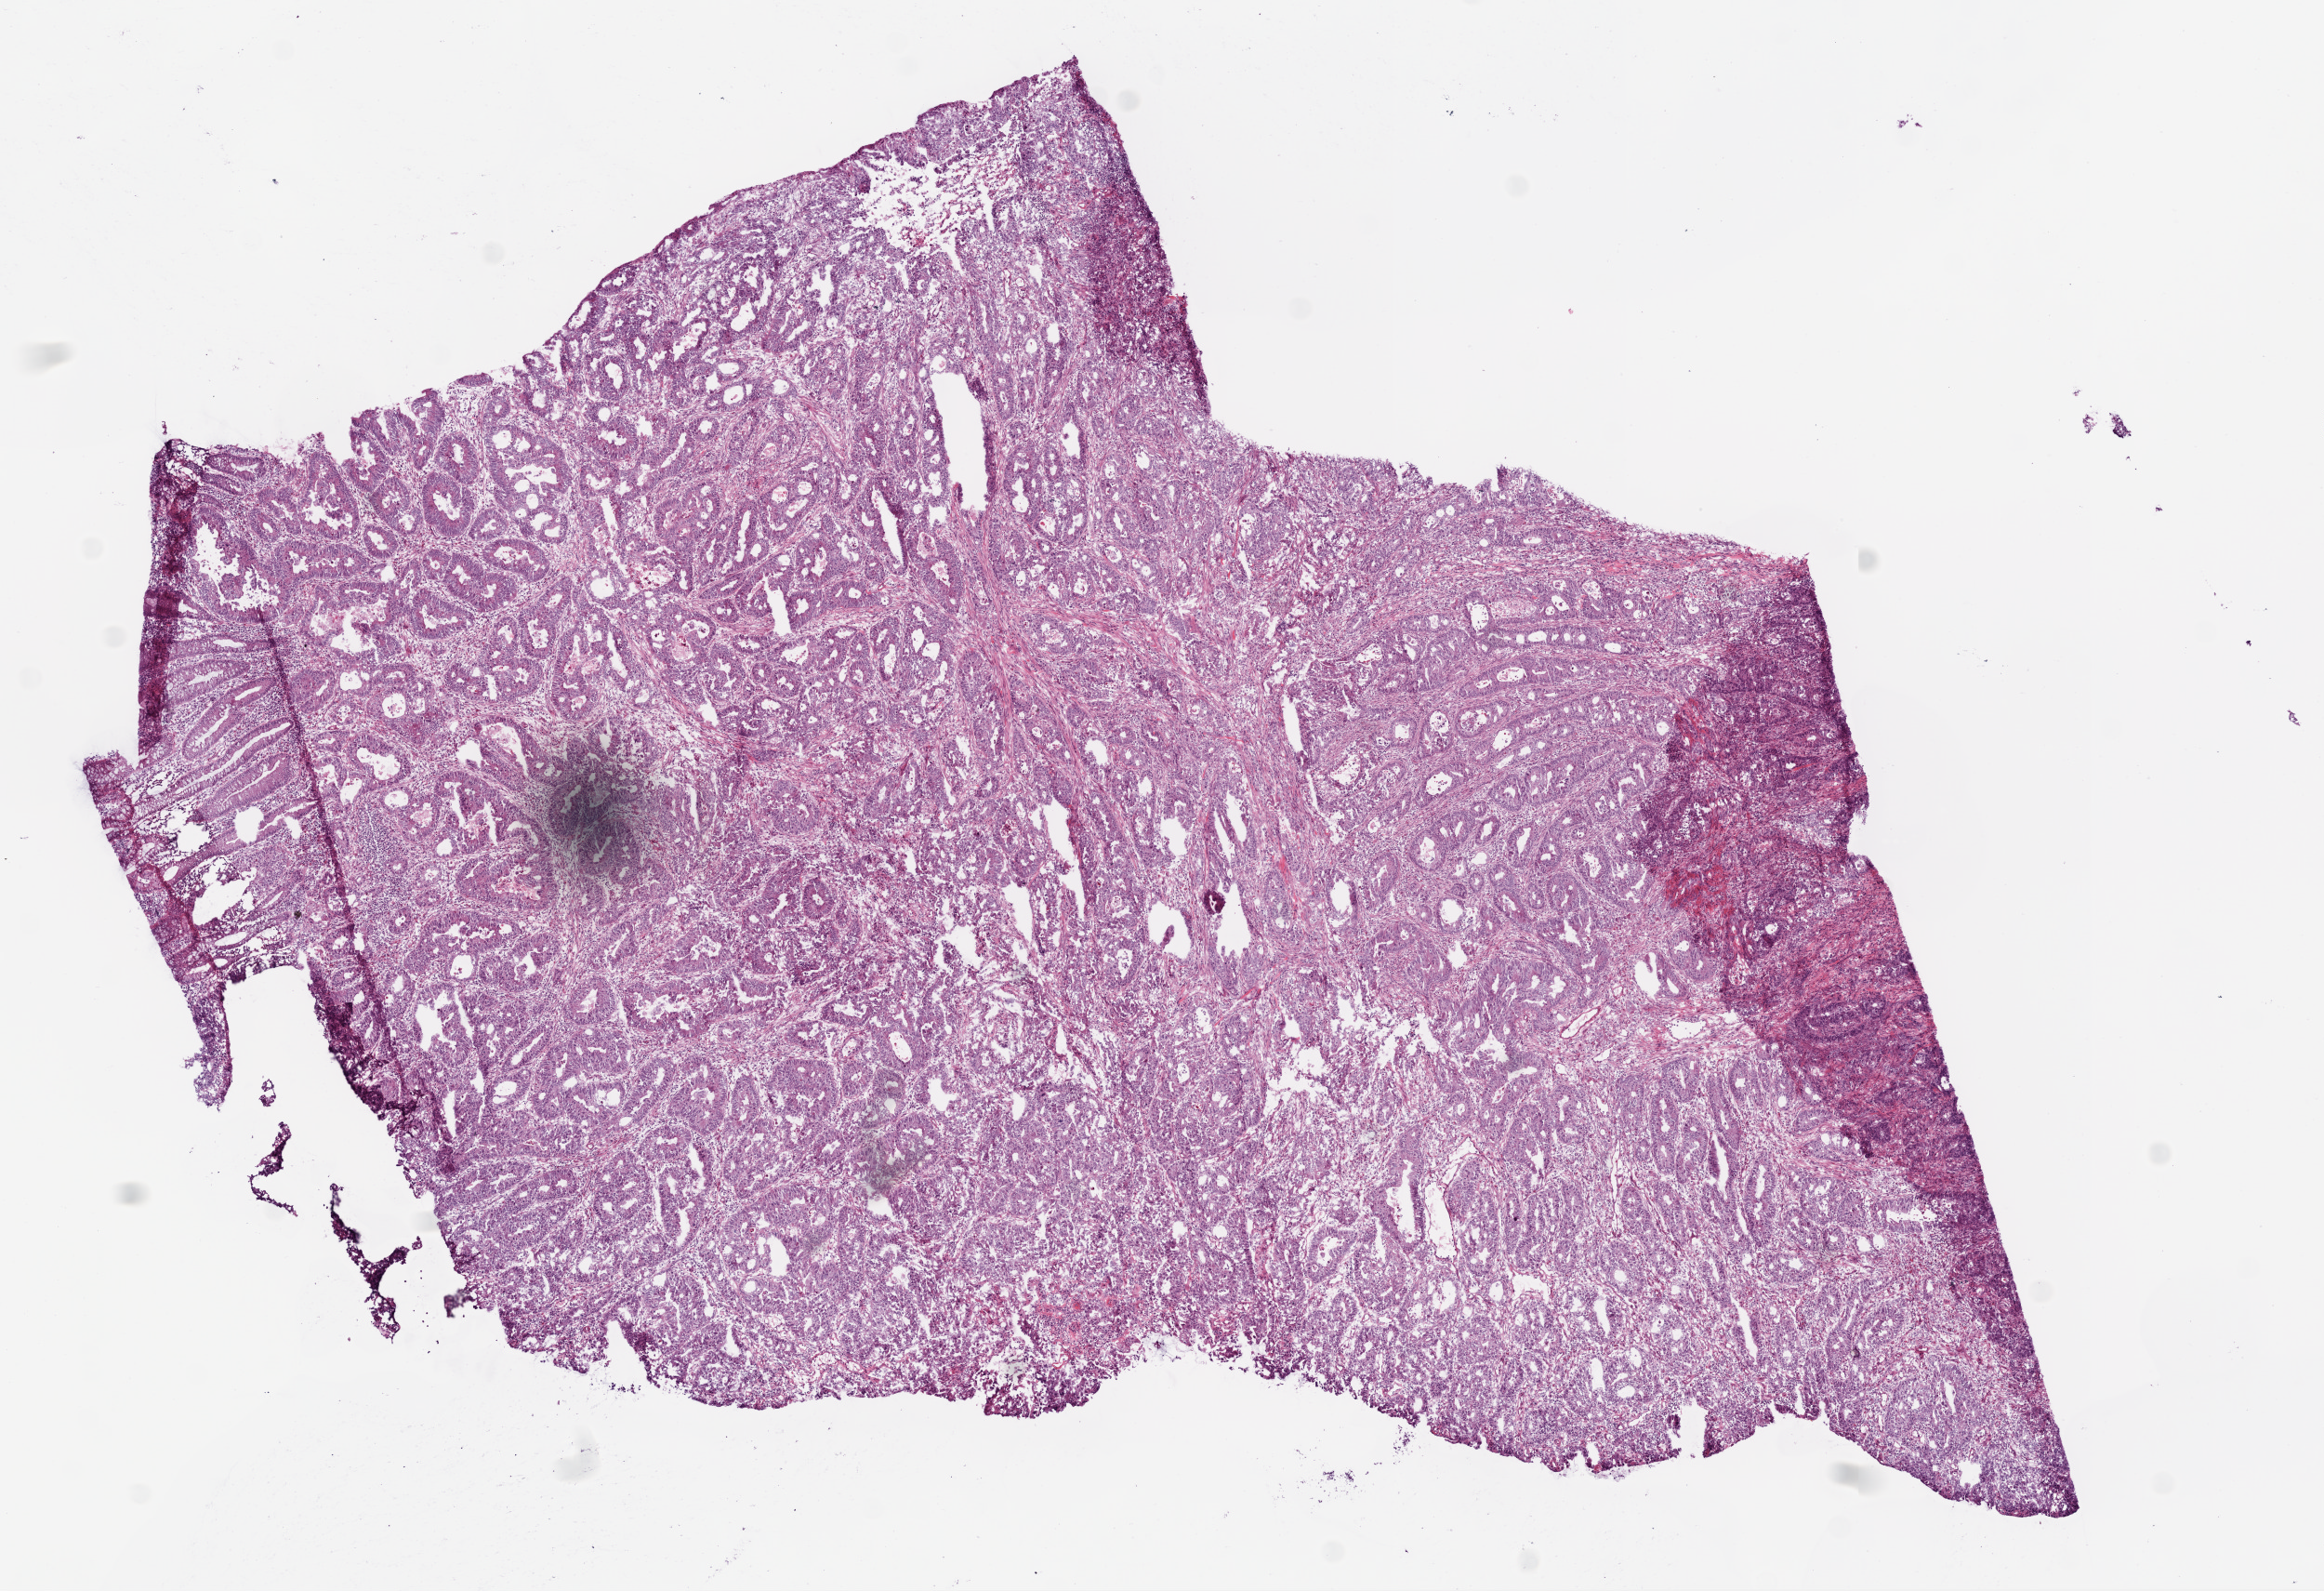
Digitized Hematoxylin and eosin (H&E) stained tissue section (whole slide), a low-resolution overview of the entire scanned area, about 10.0 x 6.9 mm (acquisition: 20x scan), frozen section from the bottom of the tissue portion, primary tumour sample from the colon. Male, age 63 years at initial diagnosis. Composition of this section per pathologist review: tumour cells 90%, tumour nuclei 95%, normal cells 0%, stromal cells 10%, necrosis 0%.
* pathologic diagnosis: Adenocarcinoma, NOS
* lymph nodes positive (case pathology): 0 of 35 examined
* AJCC pathologic stage: IIA (6th edition)